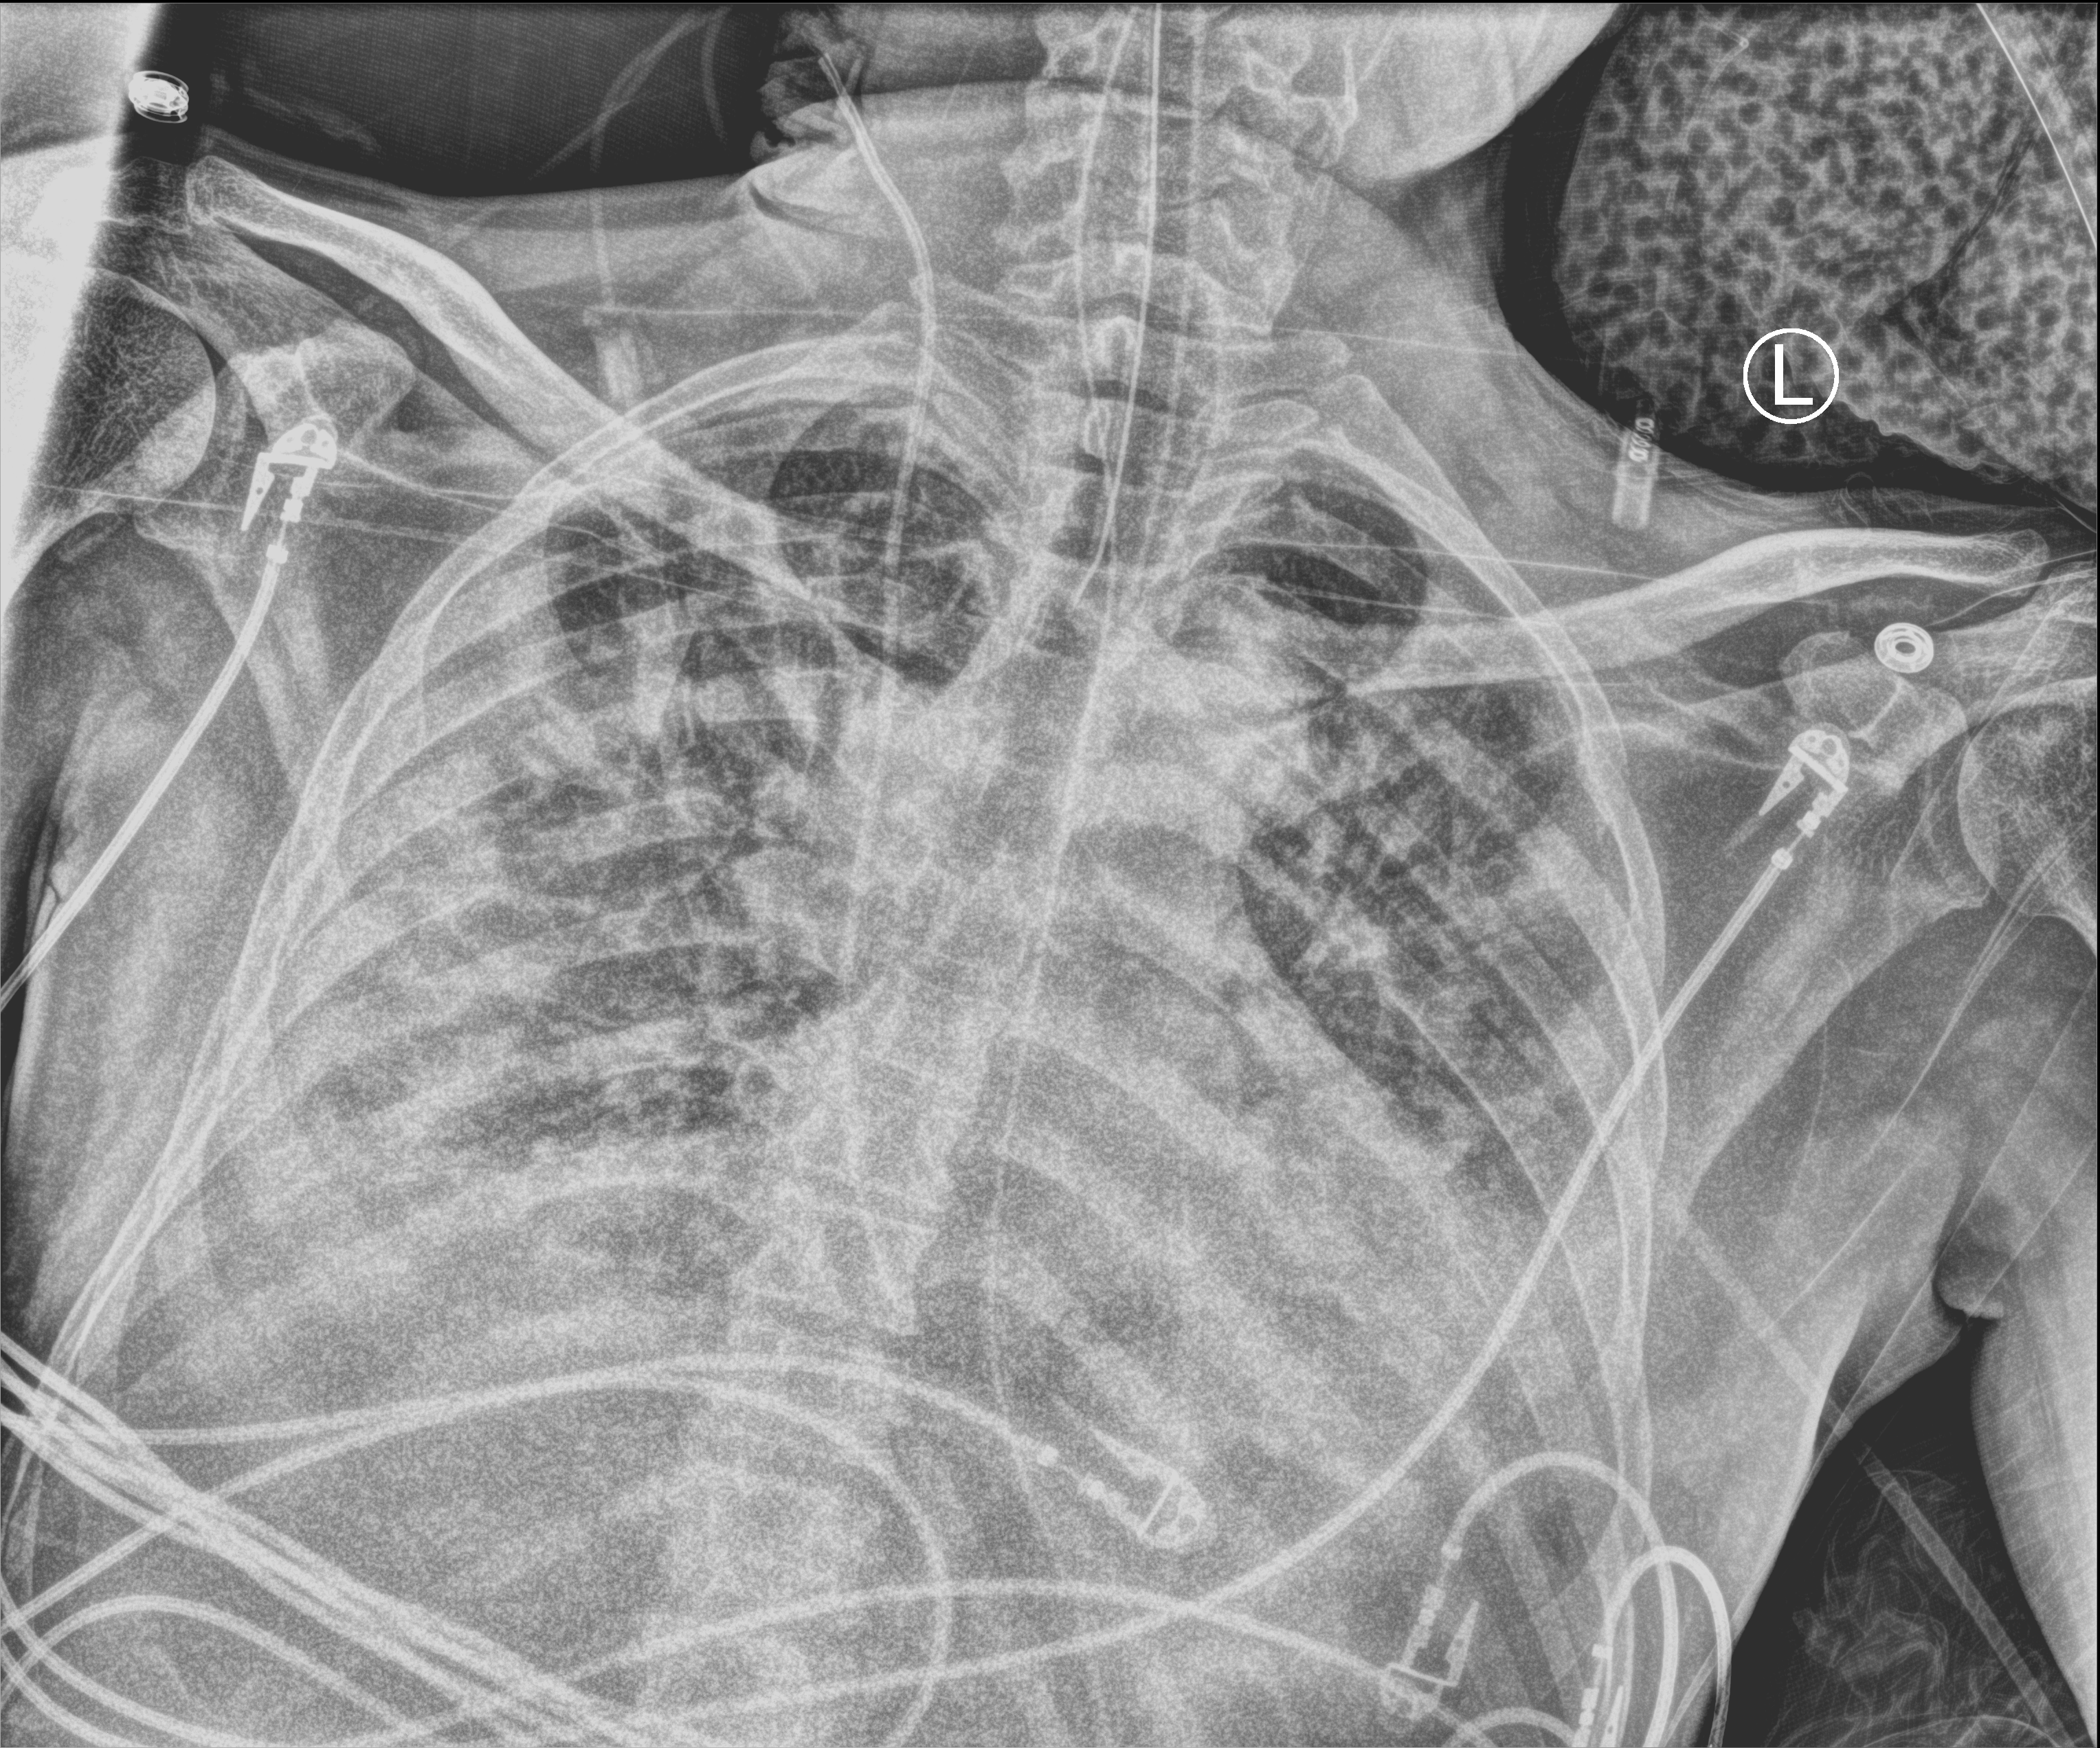
Chest X-ray (portable), anteroposterior (AP) projection. Patient hospitalised with COVID-19; male, aged 18–59 years.
Admission-level facts for this patient (not findings on this image; timing relative to this image not recorded):
- COPD (admission record): no
- admitted to intensive care during this hospital stay: yes
- smoking status (admission record): never